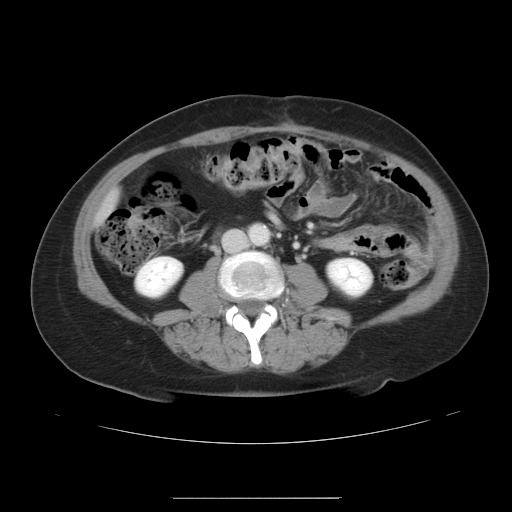
Contrast-enhanced abdominal CT, one axial slice. Slice 6 of 41 in the series (ordered by position). 120 kVp. Intravenous contrast given. Soft-tissue window (W 400 / L 40 HU). 5 mm slice thickness. 512 × 512 image matrix, field of view 381 × 381 mm. Female patient, age 63 years. Case-level facts recorded for this patient, not image findings: diagnosis: colorectal cancer liver metastases, imaged before liver resection; multiple liver metastases: yes; largest metastasis: 1.5 cm.
Structures marked on this image (expert manual segmentation):
- liver: bounding box [x1, y1, x2, y2] px = [100, 196, 116, 220]
- planned liver remnant (the part of the liver to remain after resection): [101, 196, 116, 219]